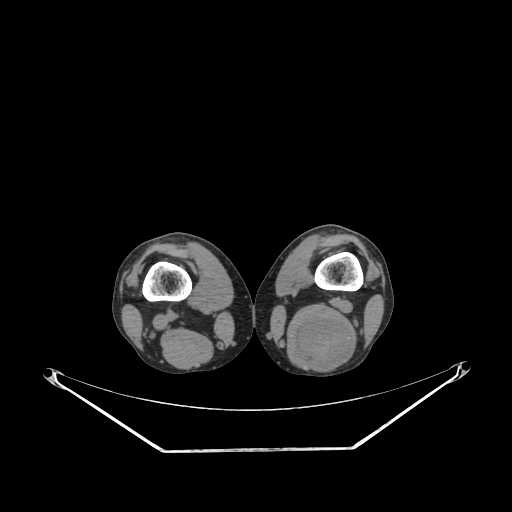
CT of an extremity soft-tissue mass (from a PET/CT study), one axial slice; position 193 of 267 along the scan axis; 140 kVp; soft-tissue window (W 400 / L 40 HU); 512 × 512 image matrix, field of view 500 × 500 mm. Male patient. Case-level facts recorded for this patient, not image findings: histological type: synovial sarcoma; site of the primary tumour: left poplietal fossa.
Structures marked on this image (expert contour drawn on MRI and transferred to this co-registered scan by the dataset authors):
- gross tumour volume (mass): box from (x=290, y=317) to (x=357, y=369) px